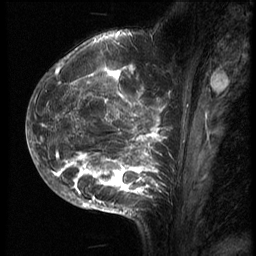
Breast MRI (dynamic contrast-enhanced), one sagittal slice; position 25 of 70 along the scan axis; 3 images stored at this slice position (order not interpretable as contrast timing); 1.5 T; TE 4.2 ms, TR 9 ms; 2.5 mm slice thickness; 256 × 256 image matrix. Female patient, age 28 years. Case-level facts recorded for this patient, not image findings: setting: breast cancer imaged before/during neoadjuvant chemotherapy.
Outlined on this slice (semi-automatic segmentation, software-assisted and operator-edited):
- analysis volume of interest (the breast-tissue region the enhancement analysis was run in; not a lesion): bounding box (x1, y1, x2, y2) in pixels: (43, 42, 186, 215)
- tumour enhancement mask (voxels above the 140 % enhancement threshold inside the analysis volume of interest): (43, 51, 171, 207)